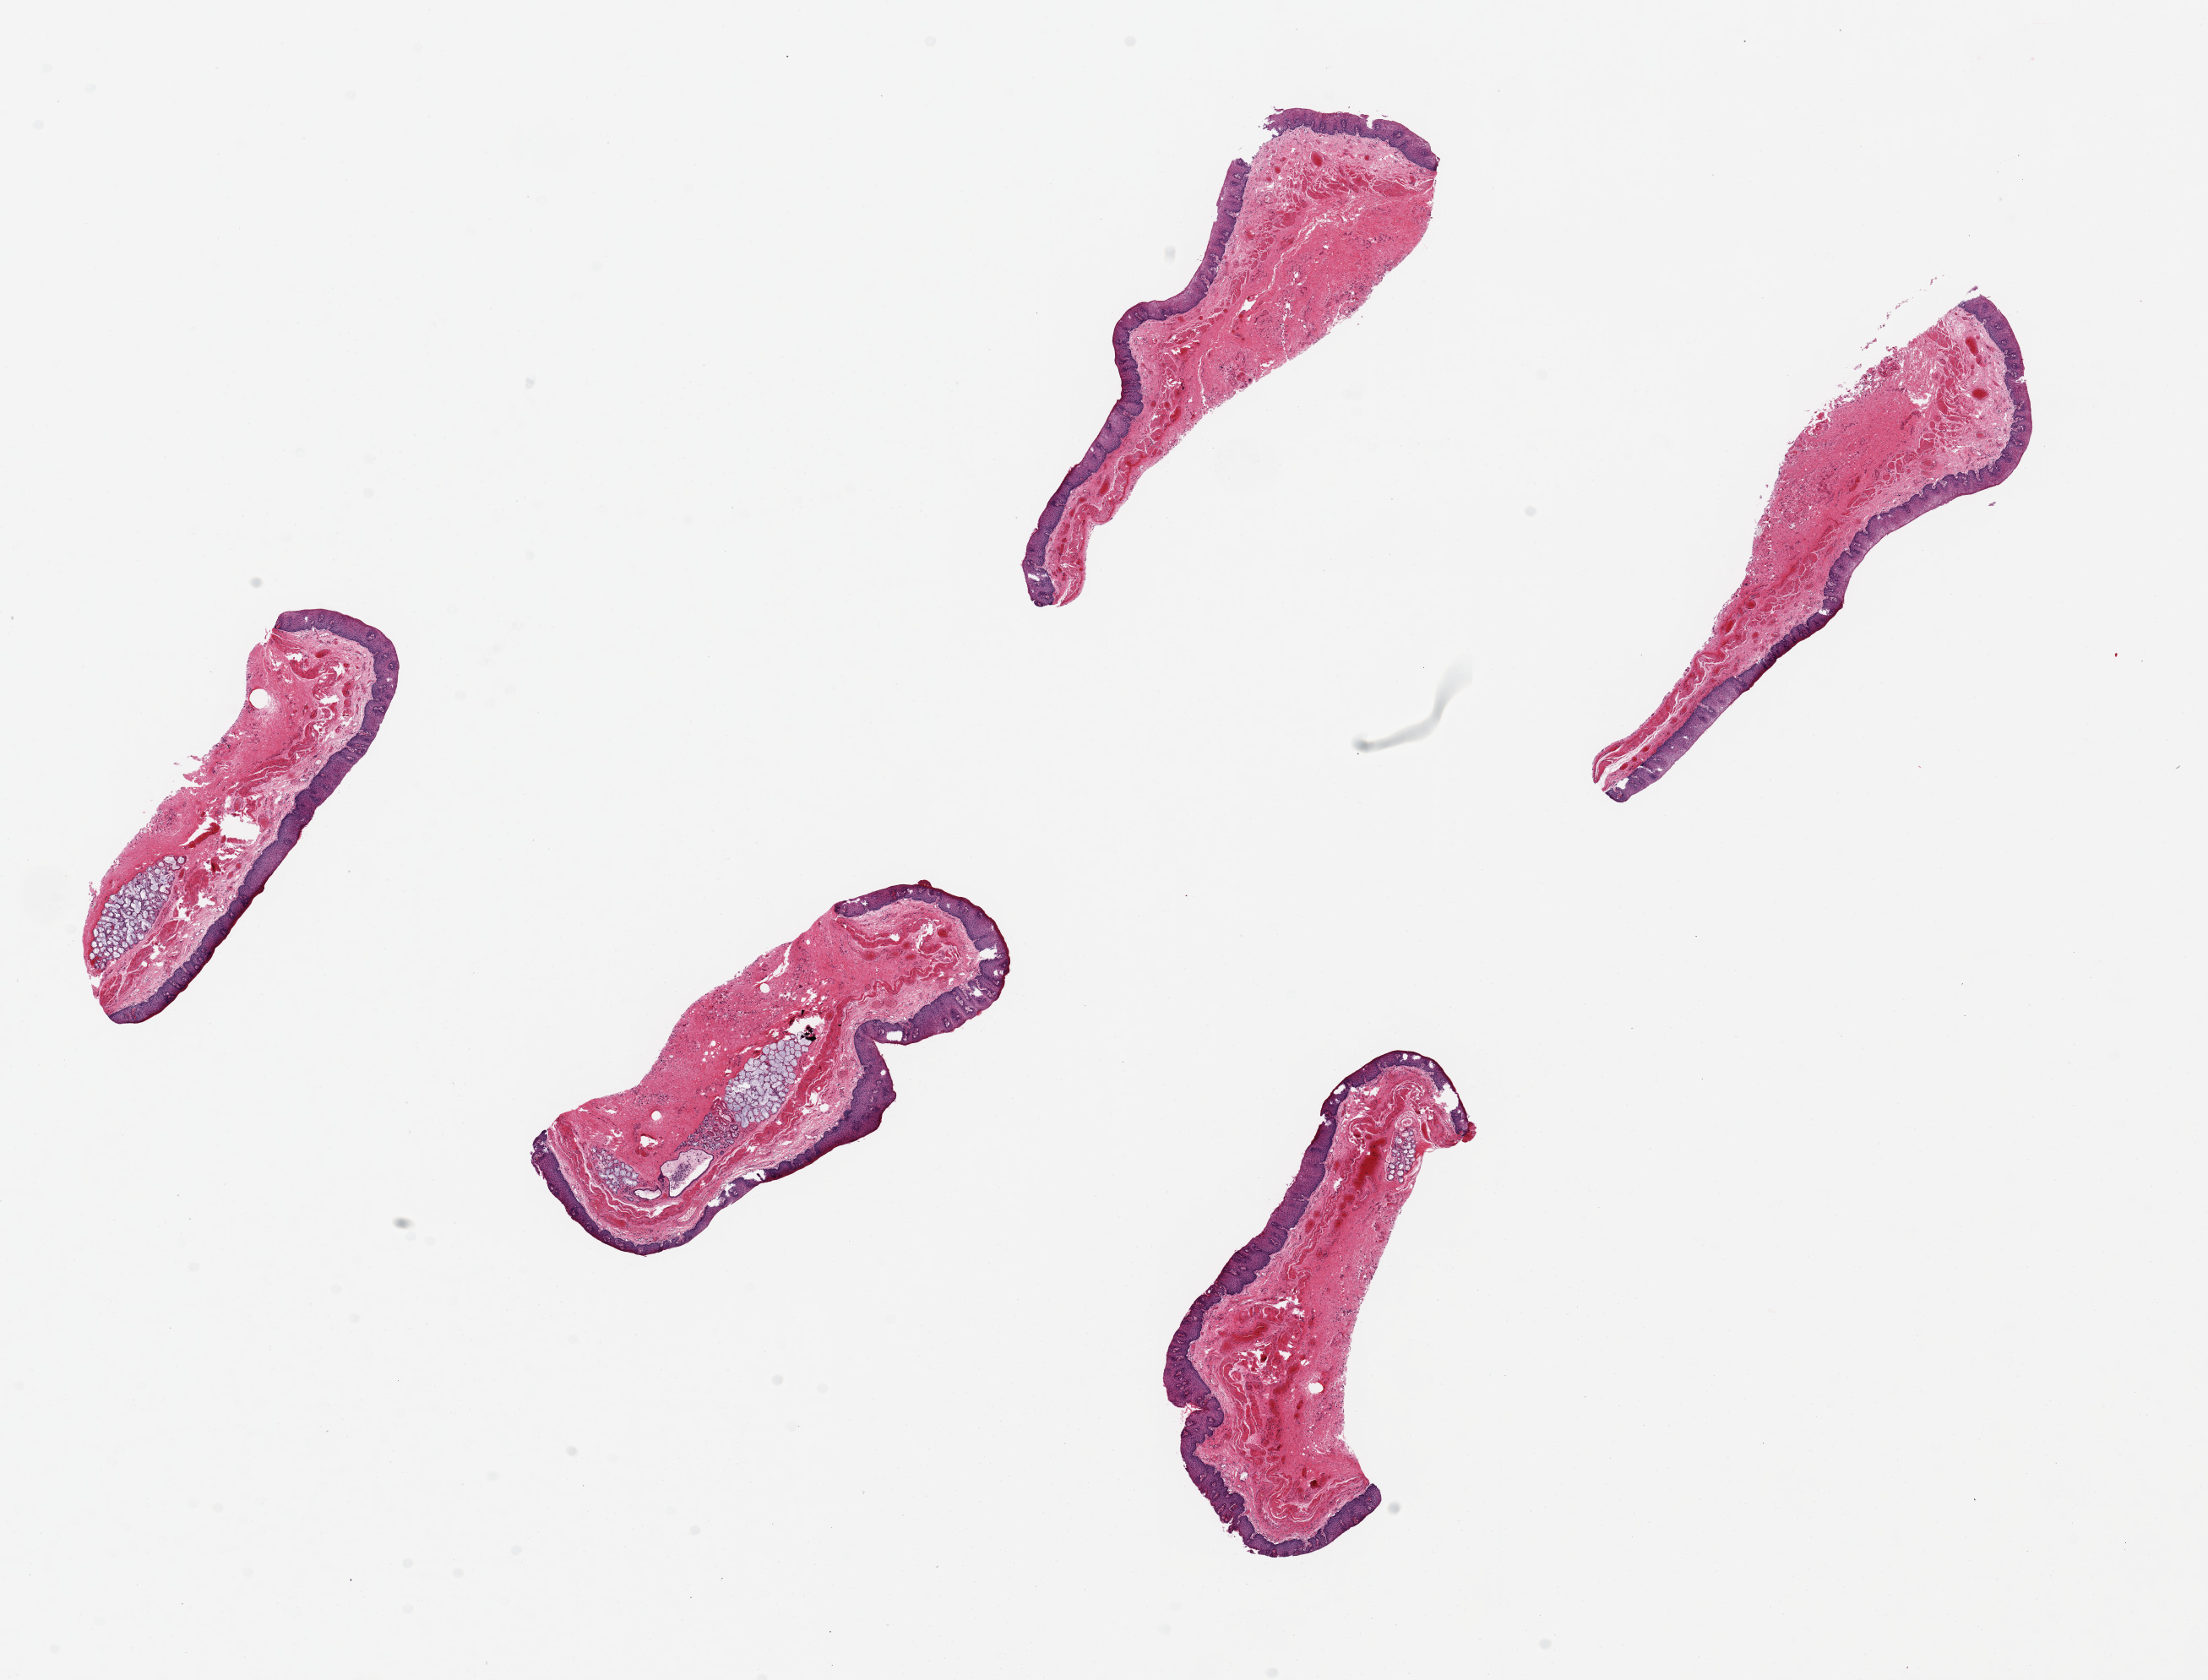
H&E whole-slide image, whole scanned area (about 20.7 x 15.7 mm, from a 20x scan) shown as a low-resolution overview; PAXgene-fixed, paraffin-embedded tissue; sampled site (target tissue): esophageal mucous membrane; tissue donor sample. Male donor.
* review note (as recorded): 5 pieces, up to 6x2mm; glands not well preserved